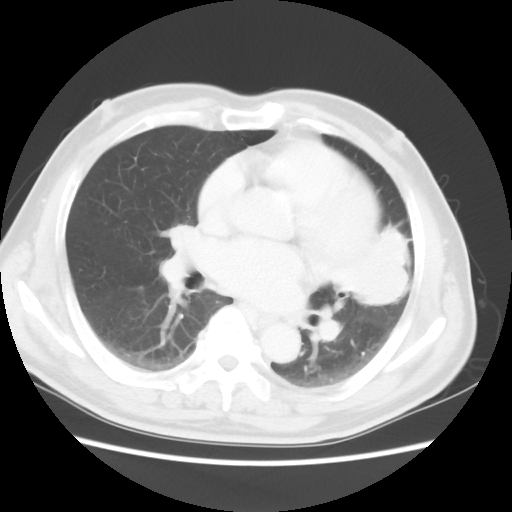
Chest CT, one axial slice; slice 24 of 50 in the series (ordered by position); reconstruction kernel STANDARD; 120 kVp; lung window (W 1500 / L -600 HU); 5 mm slice thickness; 512 × 512 image matrix, field of view 360 × 360 mm. Male patient, age 69 years. From the clinical record (not read from this slice): clinical TNM (as recorded): T3 N1 M1a.
Structures marked on this image (rectangle marked by the reading radiologist):
- lung tumour (recorded histology: squamous cell carcinoma): box from (x=344, y=221) to (x=427, y=315) px